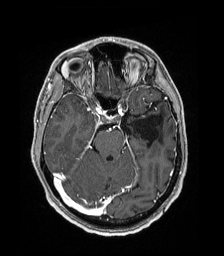
Brain MRI from a brain-tumour surgery series, one axial slice. Position 118 of 192 along the scan axis. T1-weighted post-contrast. 1 mm slice thickness. 224 × 256 image matrix. Case-level facts recorded for this patient, not image findings: histopathology: Low grade glioma; IDH mutation: no; tumour location: Left Parieto-Occipital Intraventricular.
Outlined on this slice (expert manual segmentation):
- previous resection cavity: bounding box <134,115,162,147> (left, top, right, bottom; pixels)